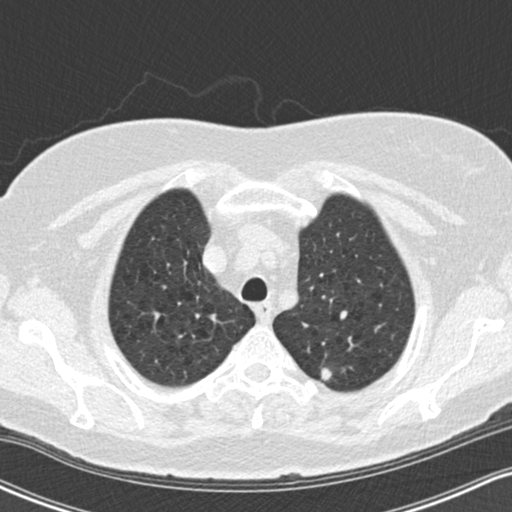
Low-dose screening chest CT, one axial slice; position 132 of 155 along the scan axis; lung window (W 1500 / L -600 HU); 2 mm slice thickness; 512 × 512 image matrix, field of view 320 × 320 mm.
Outlined on this slice (manually delineated by an expert):
- lesion 1 (tumor, upper lobe of left lung): bounding box (x1, y1, x2, y2) in pixels: (320, 367, 333, 381)